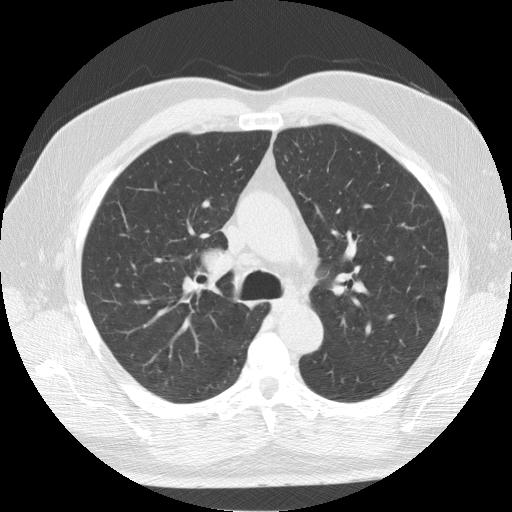
Chest CT (low-dose screening protocol), one axial image; second screening round (one year after baseline); lung window (W 1500 / L -600 HU); 512 × 512 image matrix, field of view 376 × 376 mm. Male participant, aged 64 years at enrolment. Former smoker at enrolment.
• Expert reader's lesion annotation, bounding box (x1, y1, x2, y2) in pixels: (174, 227, 251, 304).
• The exam's reader record, not a measurement of the box and not confirmed to be the same lesion: non-calcified nodule or mass ≥4 mm, right lower lobe, 7 × 5 mm, smooth margins, soft tissue attenuation, pre-existing on the prior screen: yes; interval growth: no.
• Official screen result: positive, other.
• Participant outcome: lung cancer diagnosed 63 days after this screen — adenocarcinoma, NOS, right upper lobe, poorly differentiated (G3), stage IB (AJCC 6th edition), 37 mm at pathology.